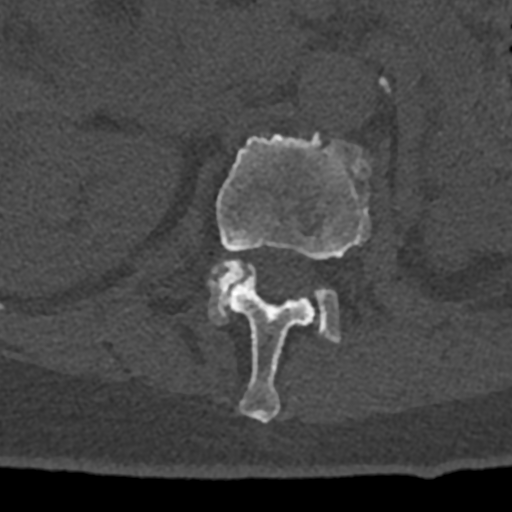
CT including the spine, one axial slice; position 420 of 797 along the scan axis; reconstruction kernel Br40s/3; 120 kVp; bone window (W 1800 / L 400 HU); 0.5 mm slice thickness; 512 × 512 image matrix, field of view 160 × 160 mm. Patient: male, 74 years. Case-level facts recorded for this patient, not image findings: primary cancer: renal; vertebrae with lytic lesions (as recorded): T10, L1, L2, L3, L4, L5.
Structures marked on this image (semi-automatically segmented with operator editing):
- L1 vertebra: box from (x=216, y=134) to (x=370, y=423) px
- L2 vertebra: (x=208, y=260)–(x=340, y=342)